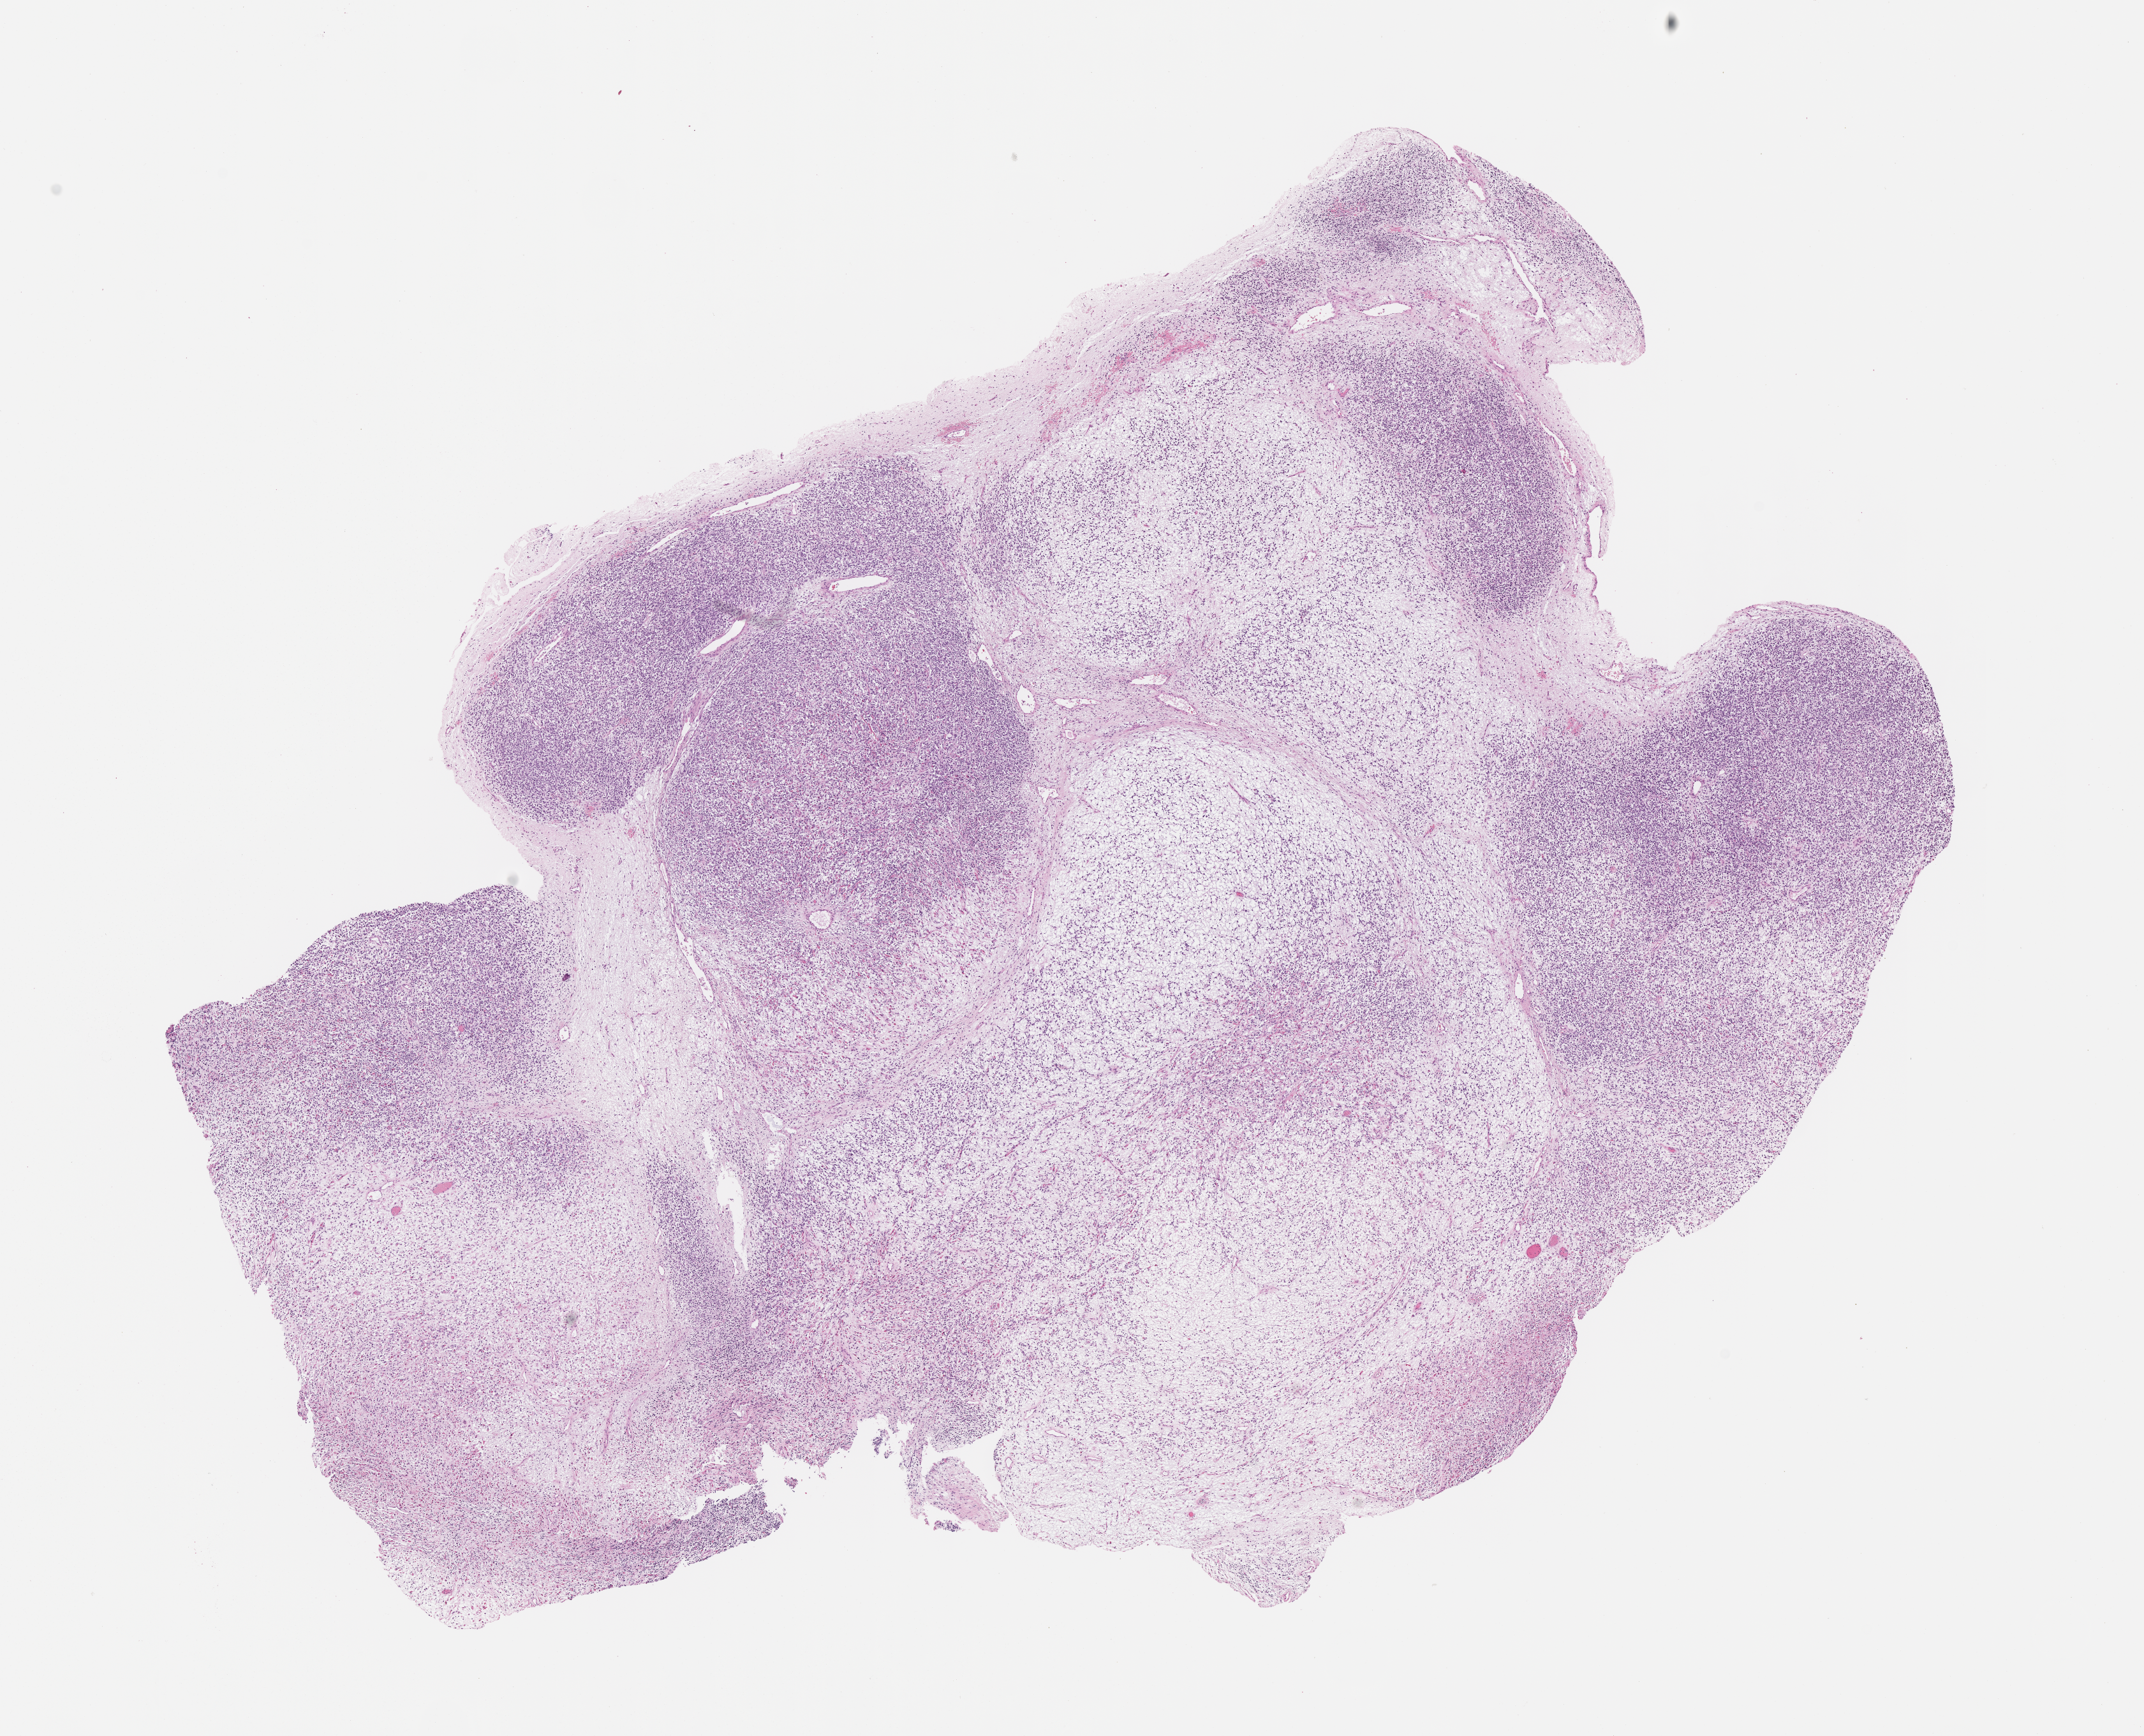
Whole-slide image, haematoxylin and eosin stain of tumor tissue, shown as a low-resolution overview of the whole scanned area (about 13.6 x 11.0 mm). Formalin-fixed, paraffin-embedded (FFPE) tissue. Sample anatomic site: abdomen. Male patient, age at diagnosis 4.0 years.
* metastatic status at presentation (as recorded): metastatic (confirmed)
* diagnosis: rhabdomyosarcoma; histological classification: embryonal rhabdomyosarcoma
* stage (as recorded): 4